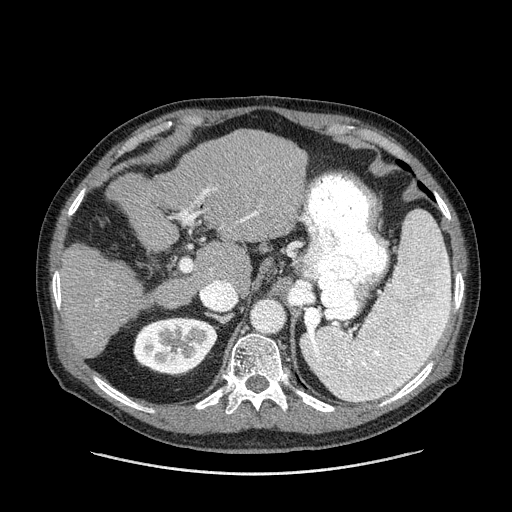
Contrast-enhanced abdominal CT (liver protocol), one axial slice. Reconstruction kernel STANDARD. One of 2 acquisitions stored at this slice position. Soft-tissue window (W 400 / L 40 HU). 2.5 mm slice thickness. 512 × 512 image matrix, field of view 420 × 420 mm. Case-level facts recorded for this patient, not image findings: diagnosis: hepatocellular carcinoma (patient treated with transarterial chemoembolisation; whether this scan precedes or follows treatment is not stated here); TNM stage (as recorded): Stage-II; Child-Pugh class: A; tumour differentiation: well differentiated; tumour nodularity: multinodular.
Structures marked on this image (semi-automatic segmentation, software-assisted and operator-edited):
- liver parenchyma outside the tumour (the mass and vessels are separate outlines, so this box may not span the whole liver): box from (x=56, y=130) to (x=306, y=358) px
- liver vessels: (x=56, y=188)–(x=258, y=308)